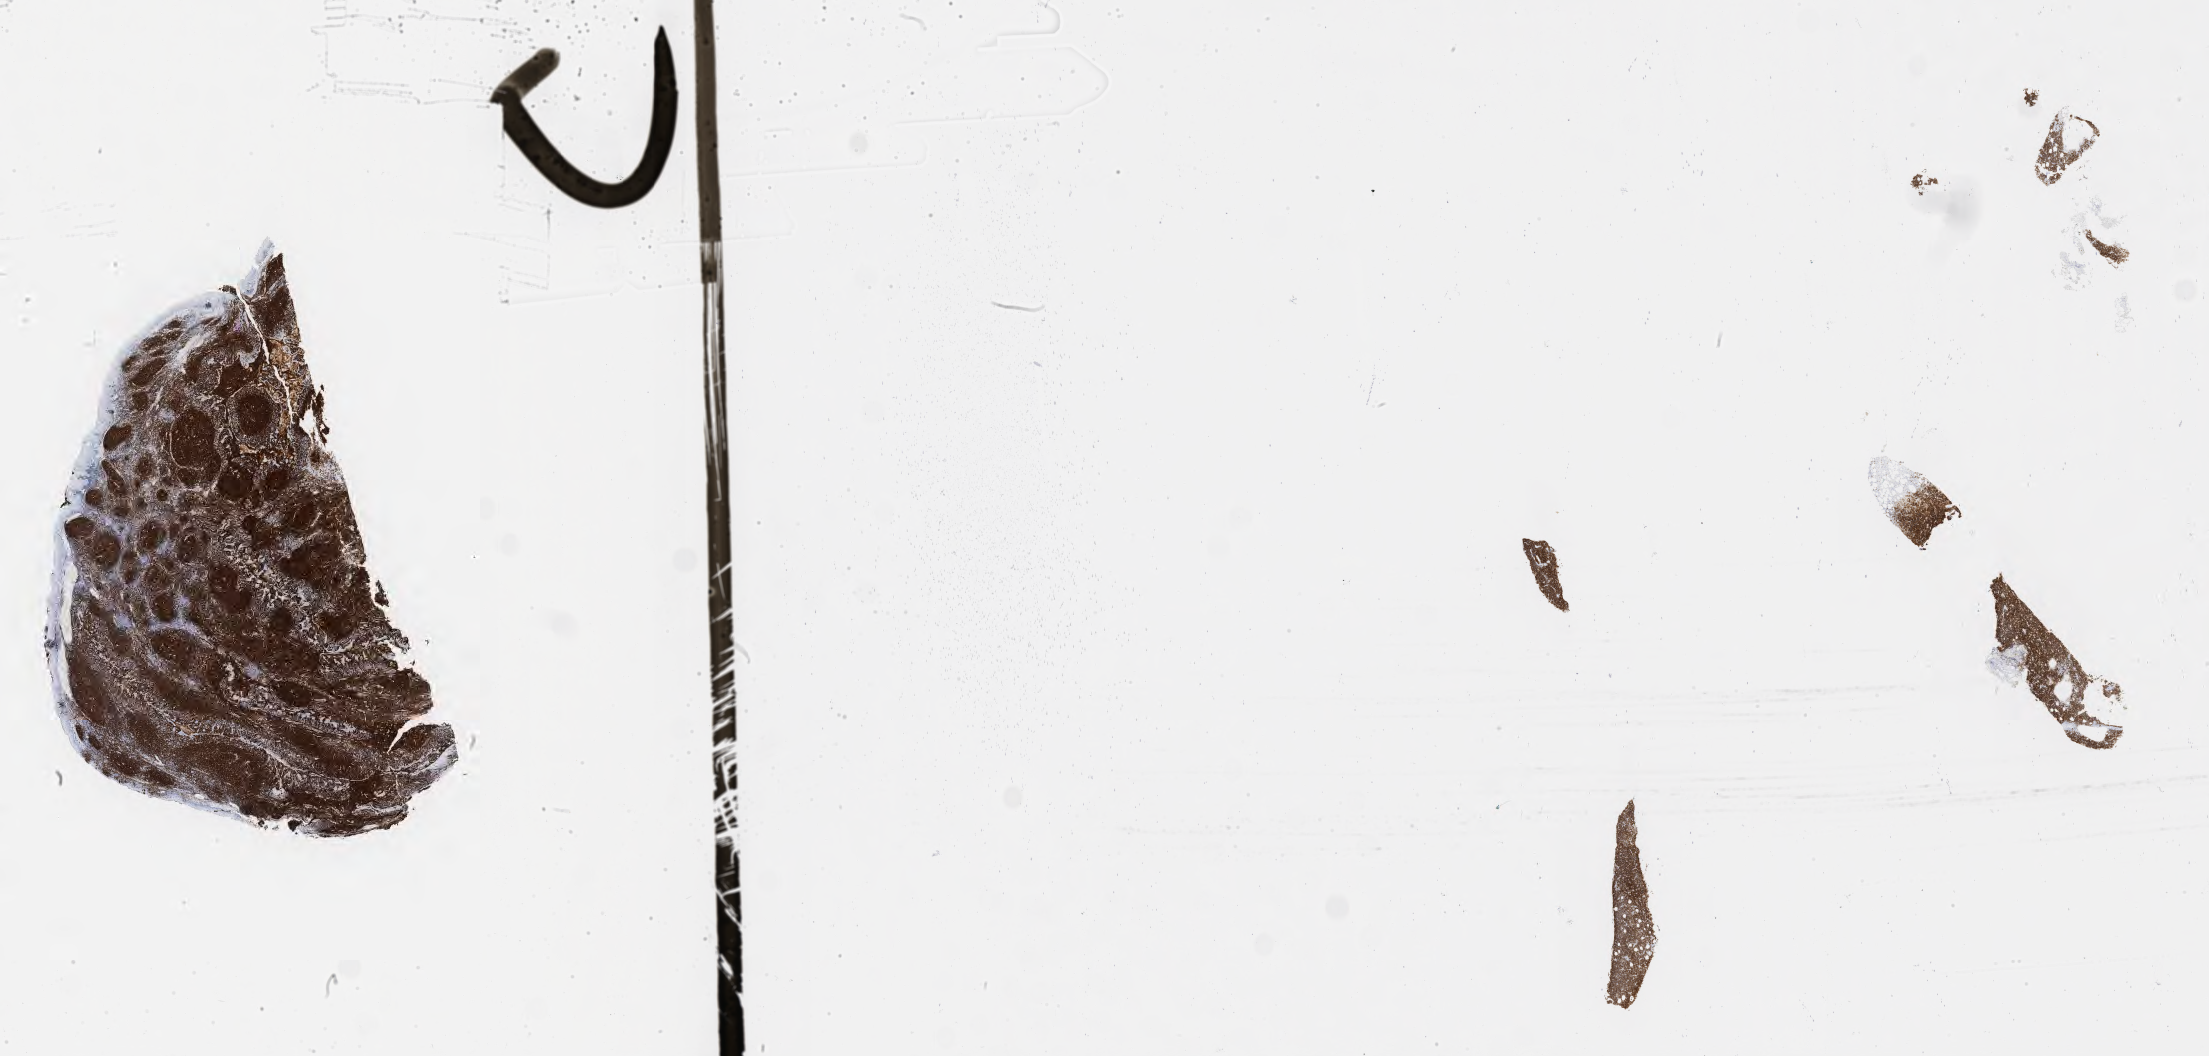
Whole-slide image, immunohistochemical stain for CD20, shown as a low-resolution overview of the whole scanned area (about 35.7 x 17.1 mm); tumor tissue. Male patient, 33 years old.
- diagnosis: Burkitt lymphoma, NOS